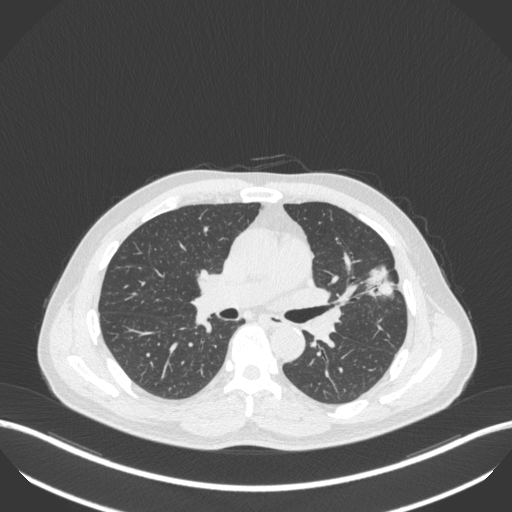
Chest CT, one axial slice. Slice 227 of 418 in the series (ordered by position). 120 kVp. Lung window (W 1500 / L -600 HU). 512 × 512 image matrix, field of view 400 × 400 mm. Male patient, age 55 years. Case-level facts recorded for this patient, not image findings: clinical TNM (as recorded): T1c N0 M0.
Outlined on this slice (bounding box drawn by a radiologist):
- lung tumour (recorded histology: adenocarcinoma): box from (x=364, y=261) to (x=399, y=298) px